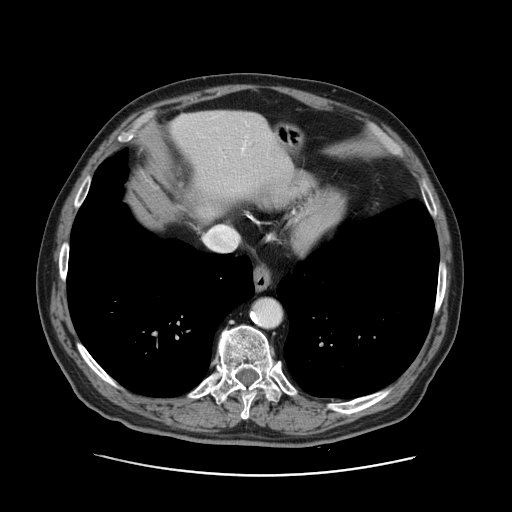
Contrast-enhanced abdominal CT, one axial slice. Slice 117 of 141 in the series (ordered by position). 120 kVp. Intravenous contrast given. Soft-tissue window (W 400 / L 40 HU). 2.5 mm slice thickness. 512 × 512 image matrix, field of view 395 × 395 mm. Male patient, age 72 years. From the clinical record (not read from this slice): diagnosis: colorectal cancer liver metastases, imaged before liver resection; multiple liver metastases: yes; largest metastasis: 5.4 cm; disease in both lobes: yes.
Annotated regions visible in this slice (manually delineated by an expert):
- hepatic veins: bounding box [x1, y1, x2, y2] px = [241, 146, 245, 152]
- liver: [170, 110, 289, 210]
- planned liver remnant (the part of the liver to remain after resection): [170, 110, 290, 204]